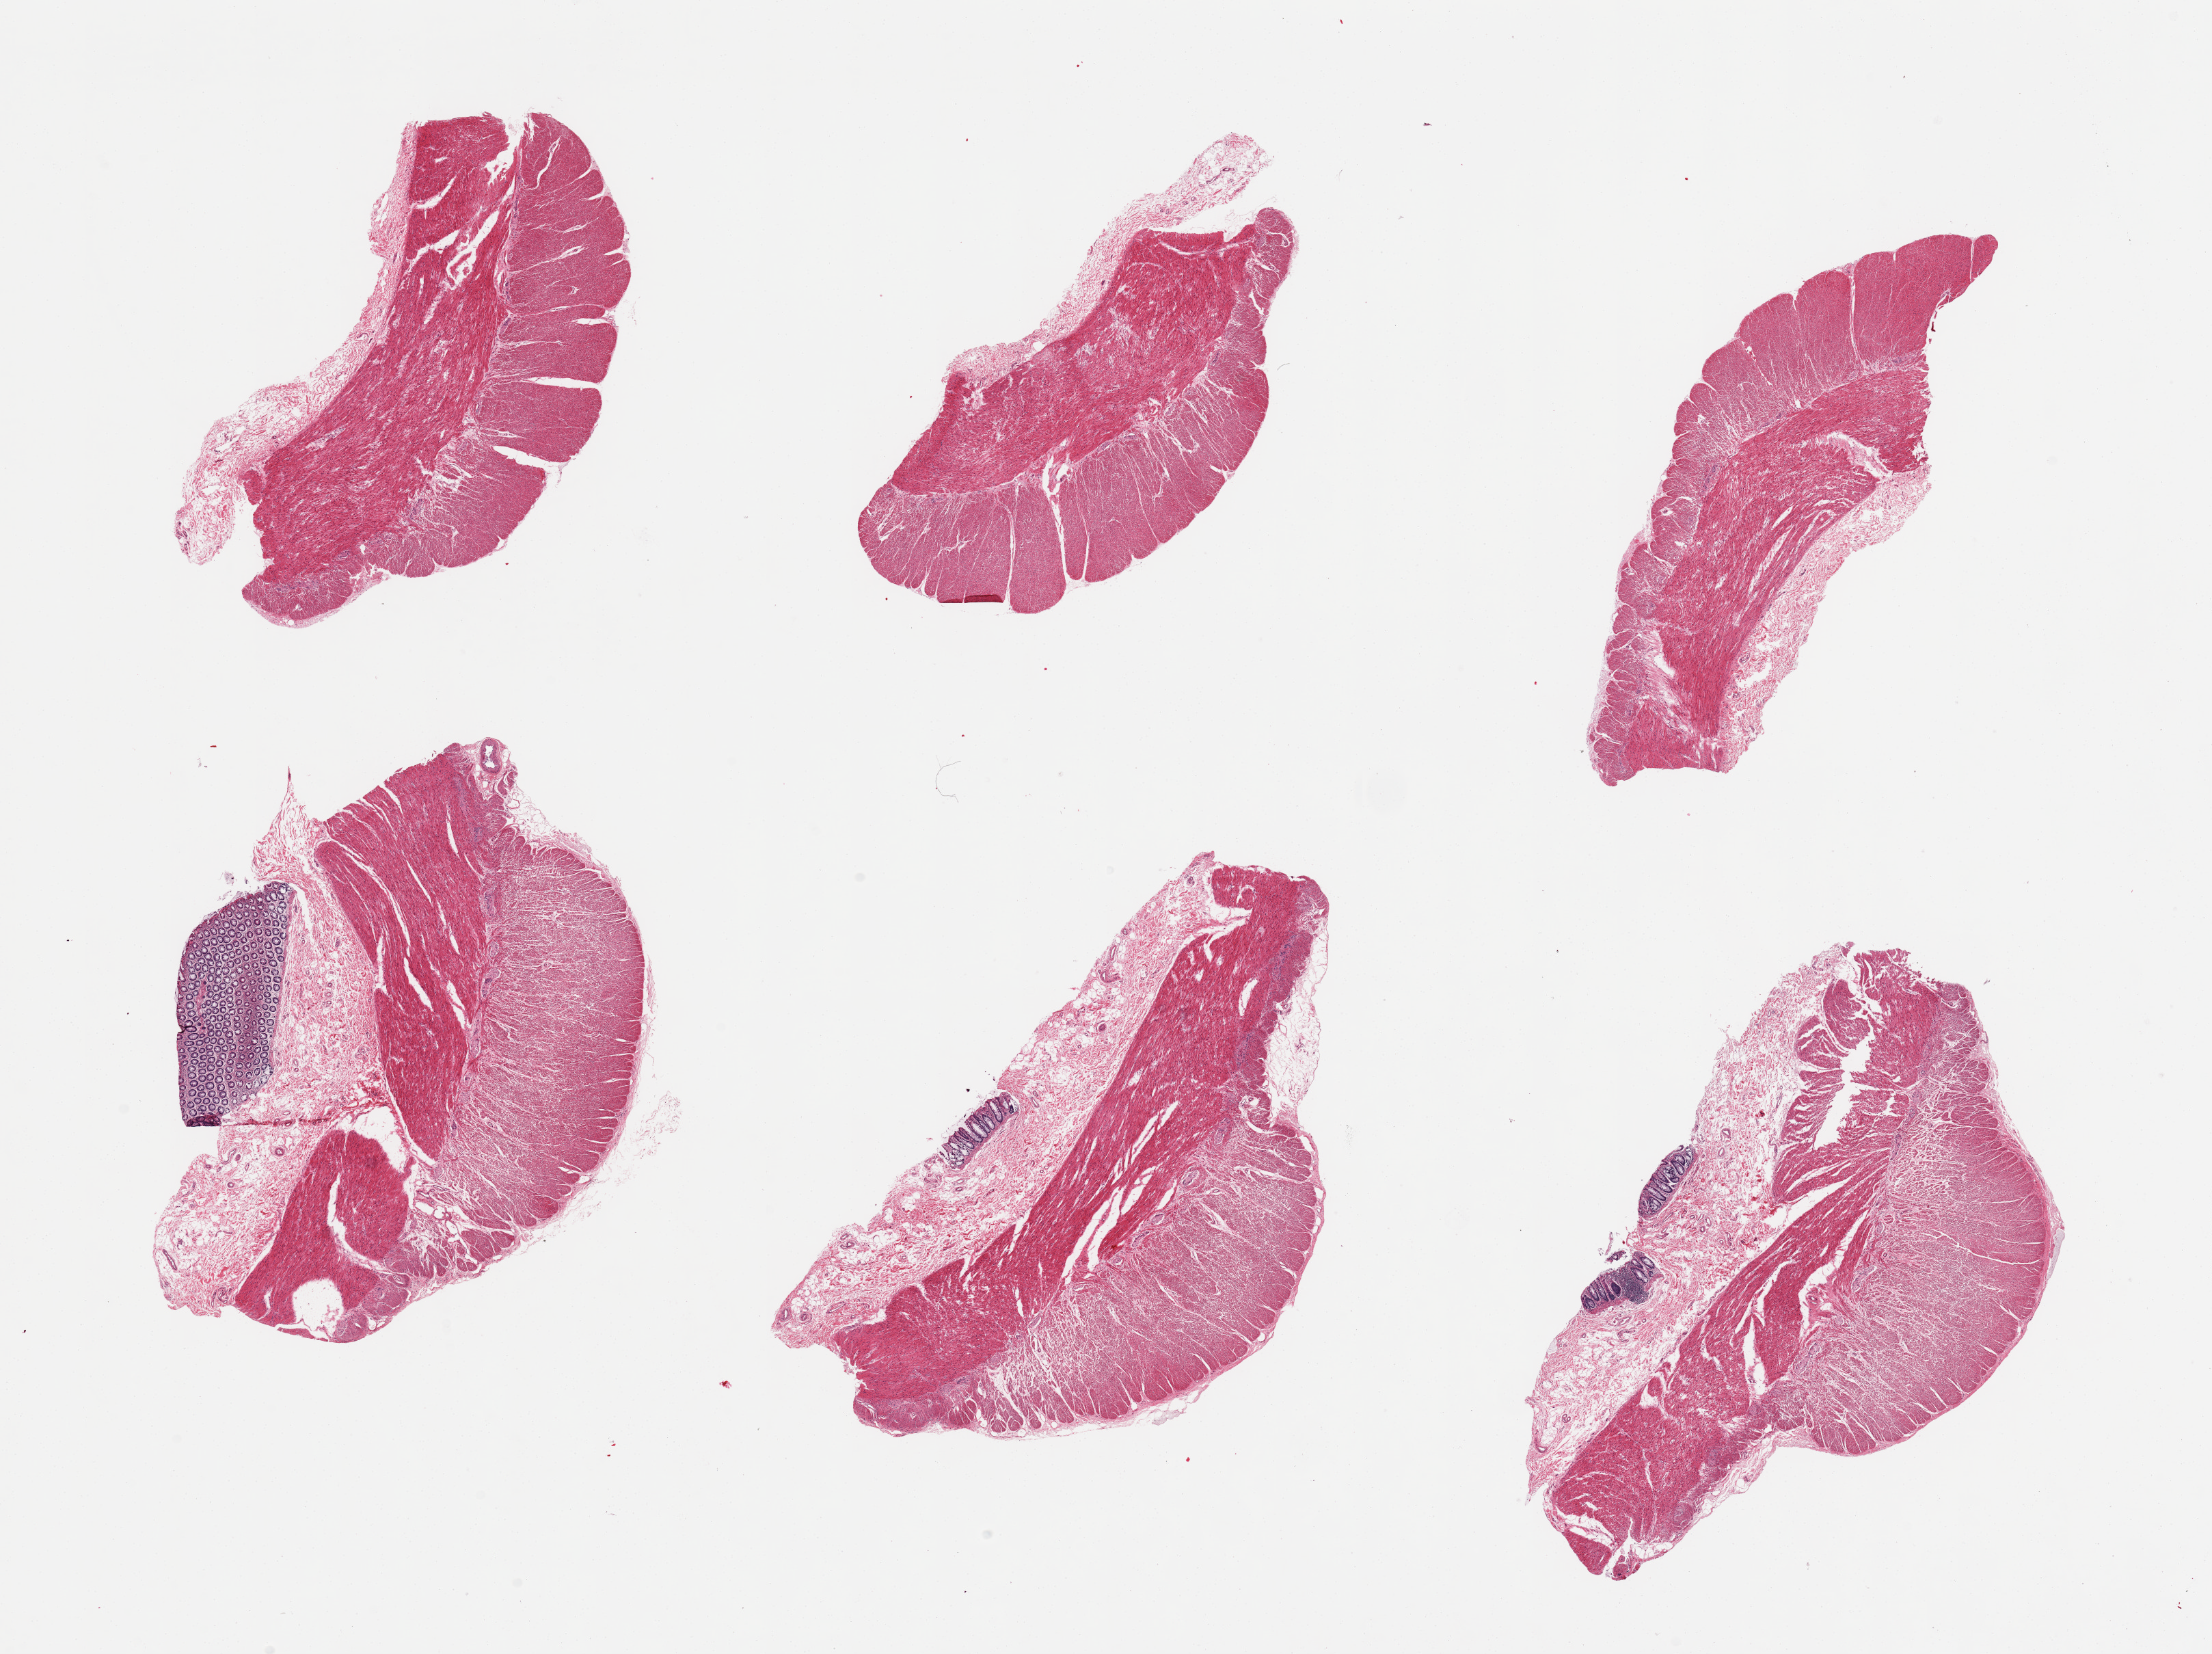
Hematoxylin and eosin (H&E) whole-slide image, brightfield — whole scanned area (about 25.6 x 19.1 mm) shown as a low-resolution overview. PAXgene-fixed paraffin-embedded (PFPE) section. Section of transverse colon (target tissue). Tissue donor sample. Donor sex: female.
* reviewer comment on this tissue sample: 6 pieces, 3 are muscularis only and 3 are predominantly muscularis, each with small strip of mucosa